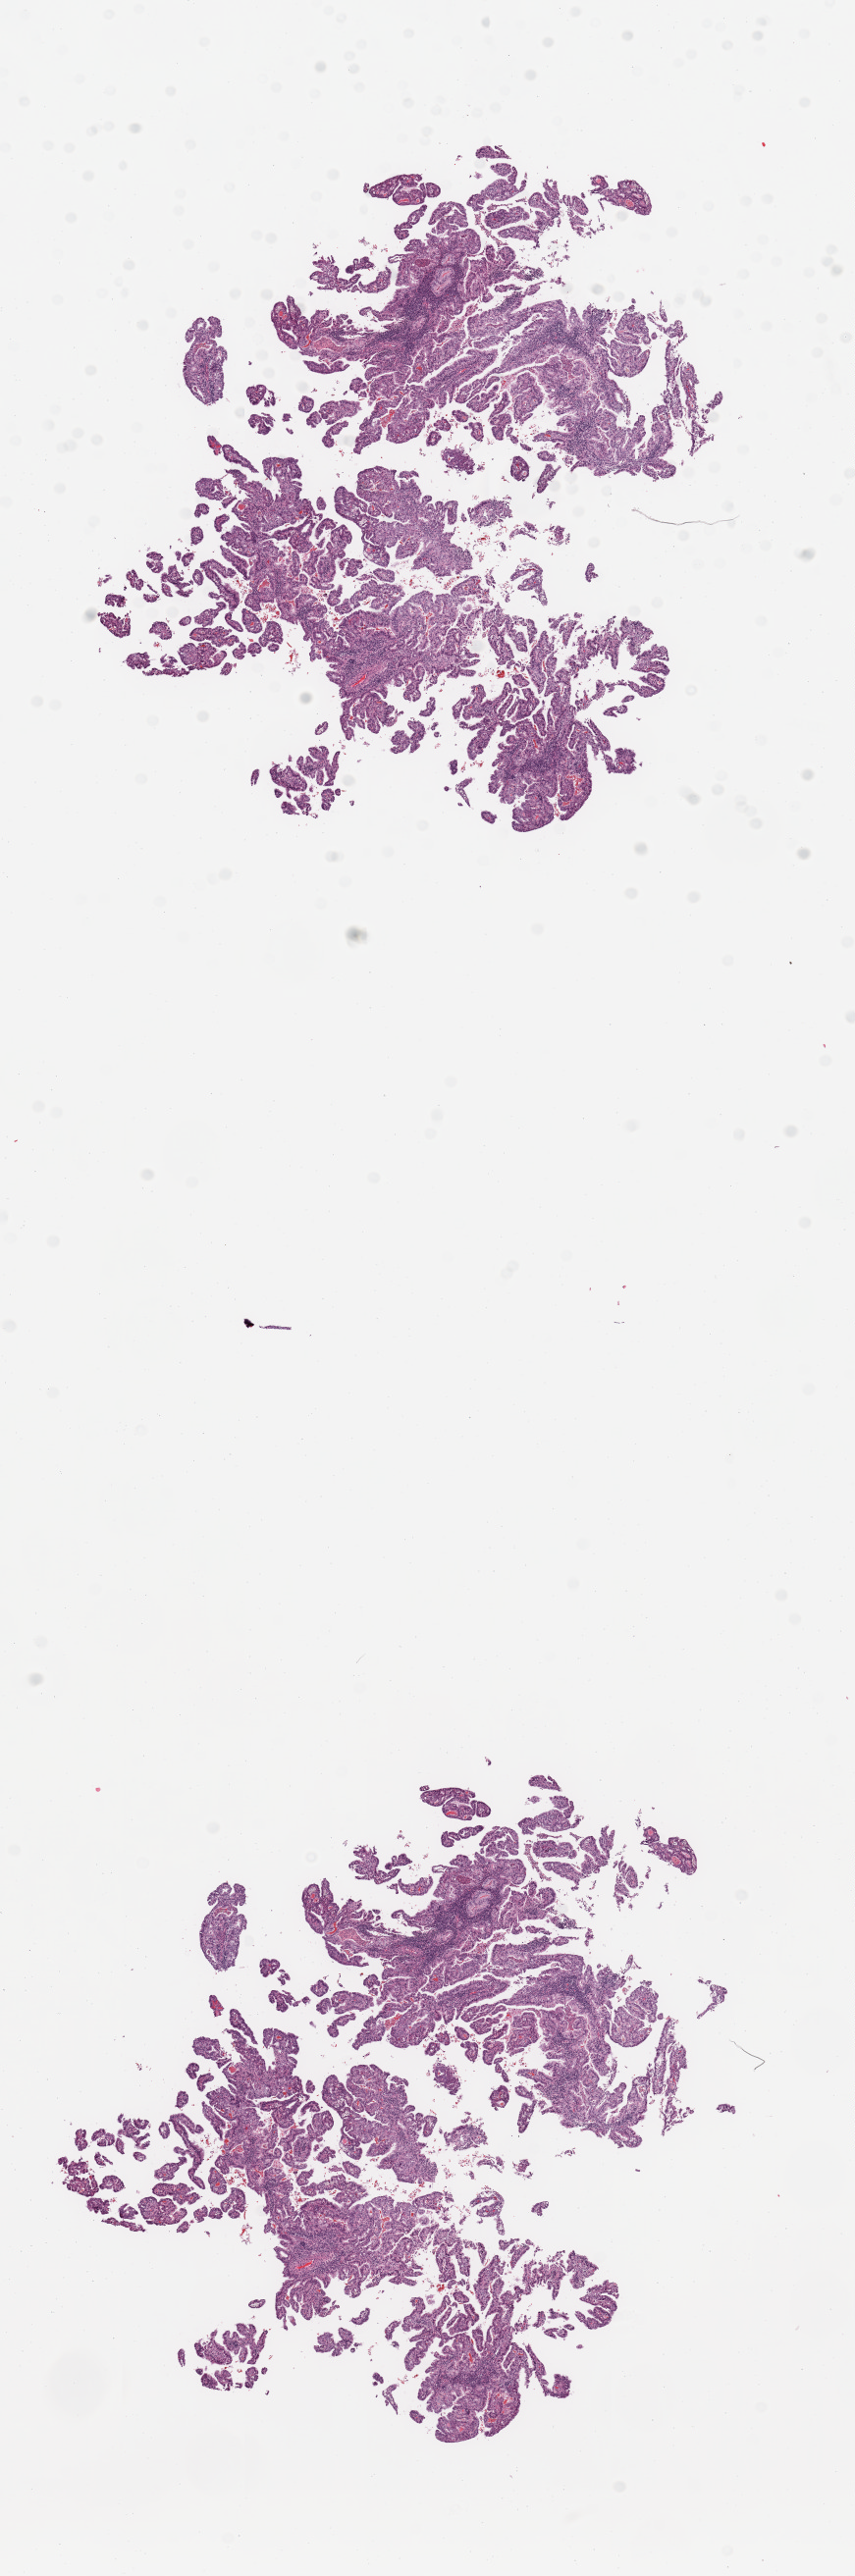
Whole-slide histology image, H&E-stained, shown as a low-resolution overview of the whole scanned area (about 6.9 x 20.8 mm). Uterus, tumour tissue. Patient: female, age 69 years. Histologic grade: G1 (well differentiated).
- AJCC pathologic stage: I
- histologic diagnosis: Endometrioid adenocarcinoma, NOS